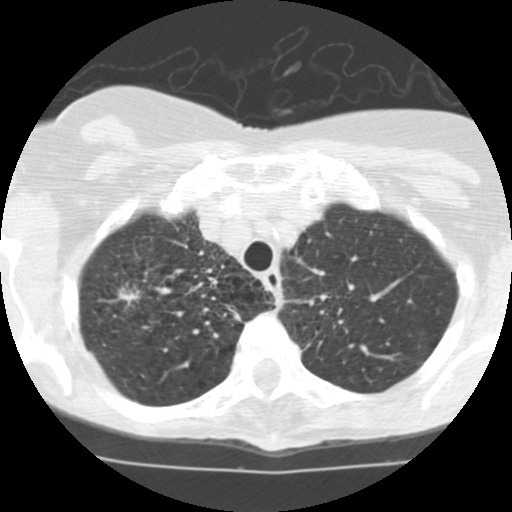
Low-dose screening chest CT, axial slice; second screening round (one year after baseline); lung window (W 1500 / L -600 HU); 2.5 mm slice thickness; slice 22 of 115 in the series; 512 × 512 image matrix, field of view 280 × 280 mm. Female, age 68 years at enrolment.
• Expert reader's lesion annotation, bounding box <83,266,155,339> (left, top, right, bottom; pixels).
• The screening reader recorded 3 non-calcified nodules or masses ≥4 mm on this exam (right upper lobe, right upper lobe, right middle lobe); which of them this box marks is not recorded.
• Official screen result: positive, other.
• Lung cancer was diagnosed 36 days after this screen: large cell neuroendocrine carcinoma, right upper lobe, undifferentiated (G4), stage IB (AJCC 6th edition), 22 mm at pathology.